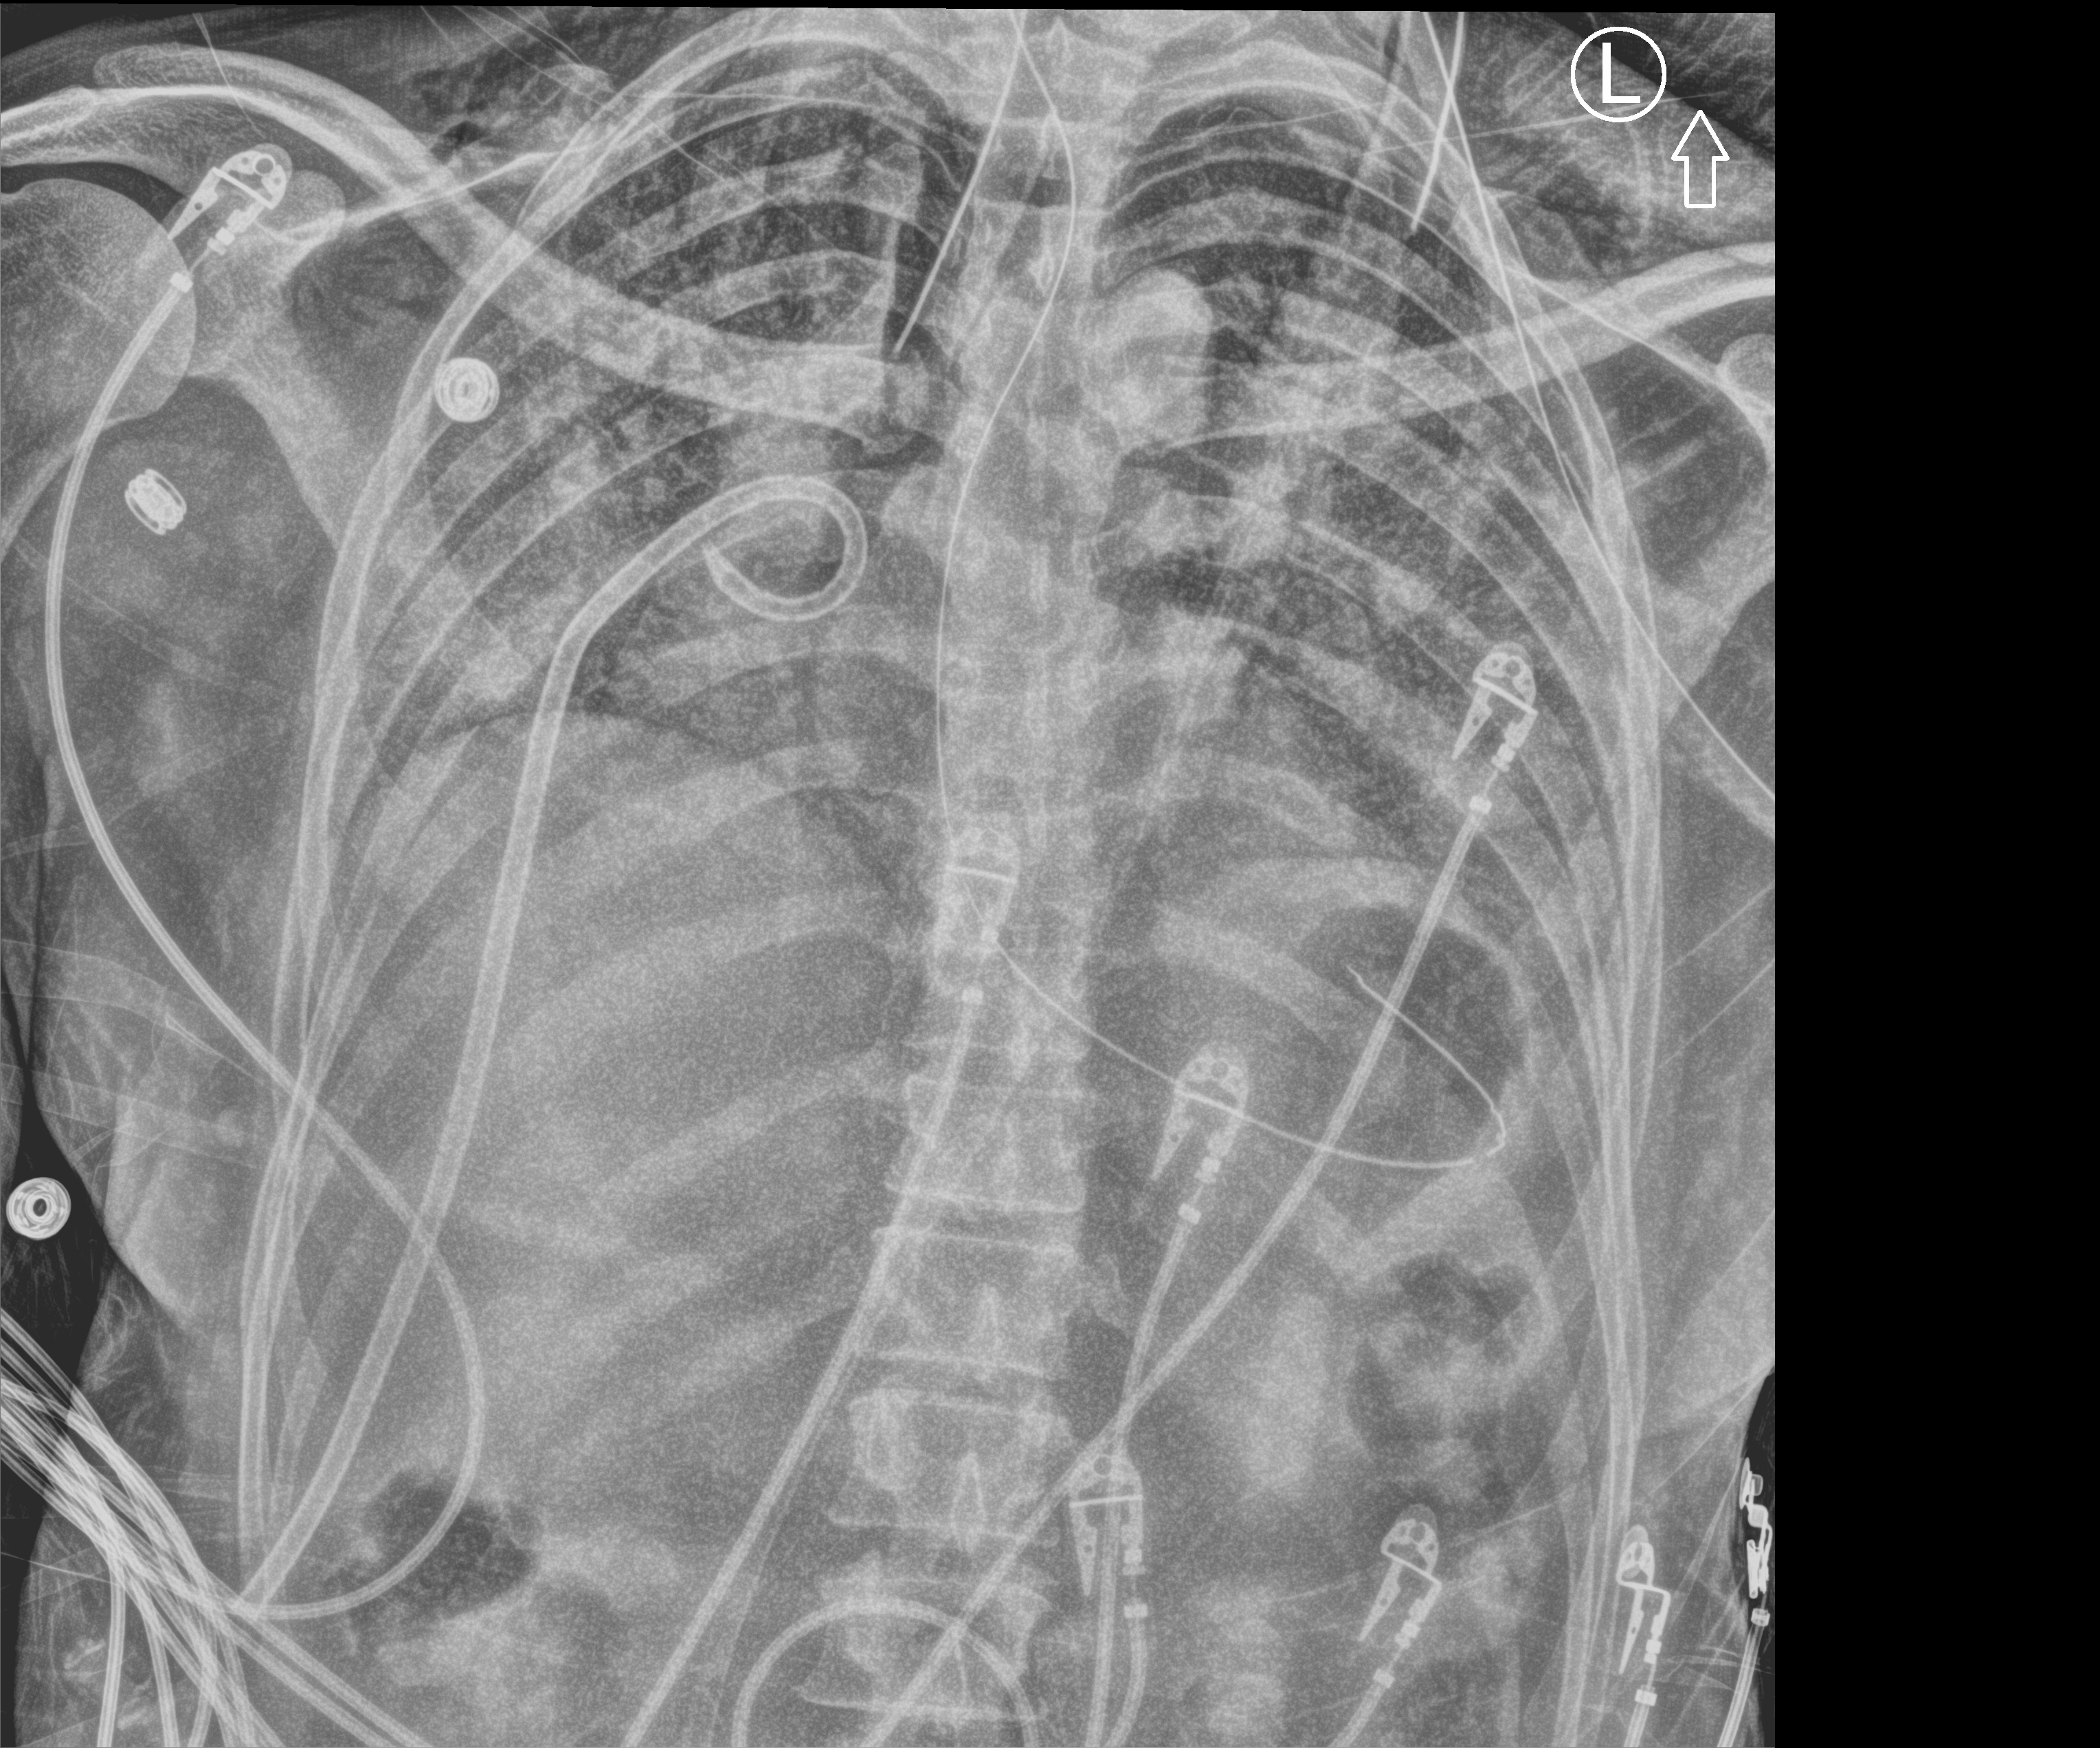
Bedside chest radiograph (computed radiography), anteroposterior (AP) projection. Adult patient hospitalised with COVID-19, age 18–59 years.
From the hospital-stay record, not from the radiograph (when in the stay this image was taken is not recorded): length of hospital stay: 41 days.